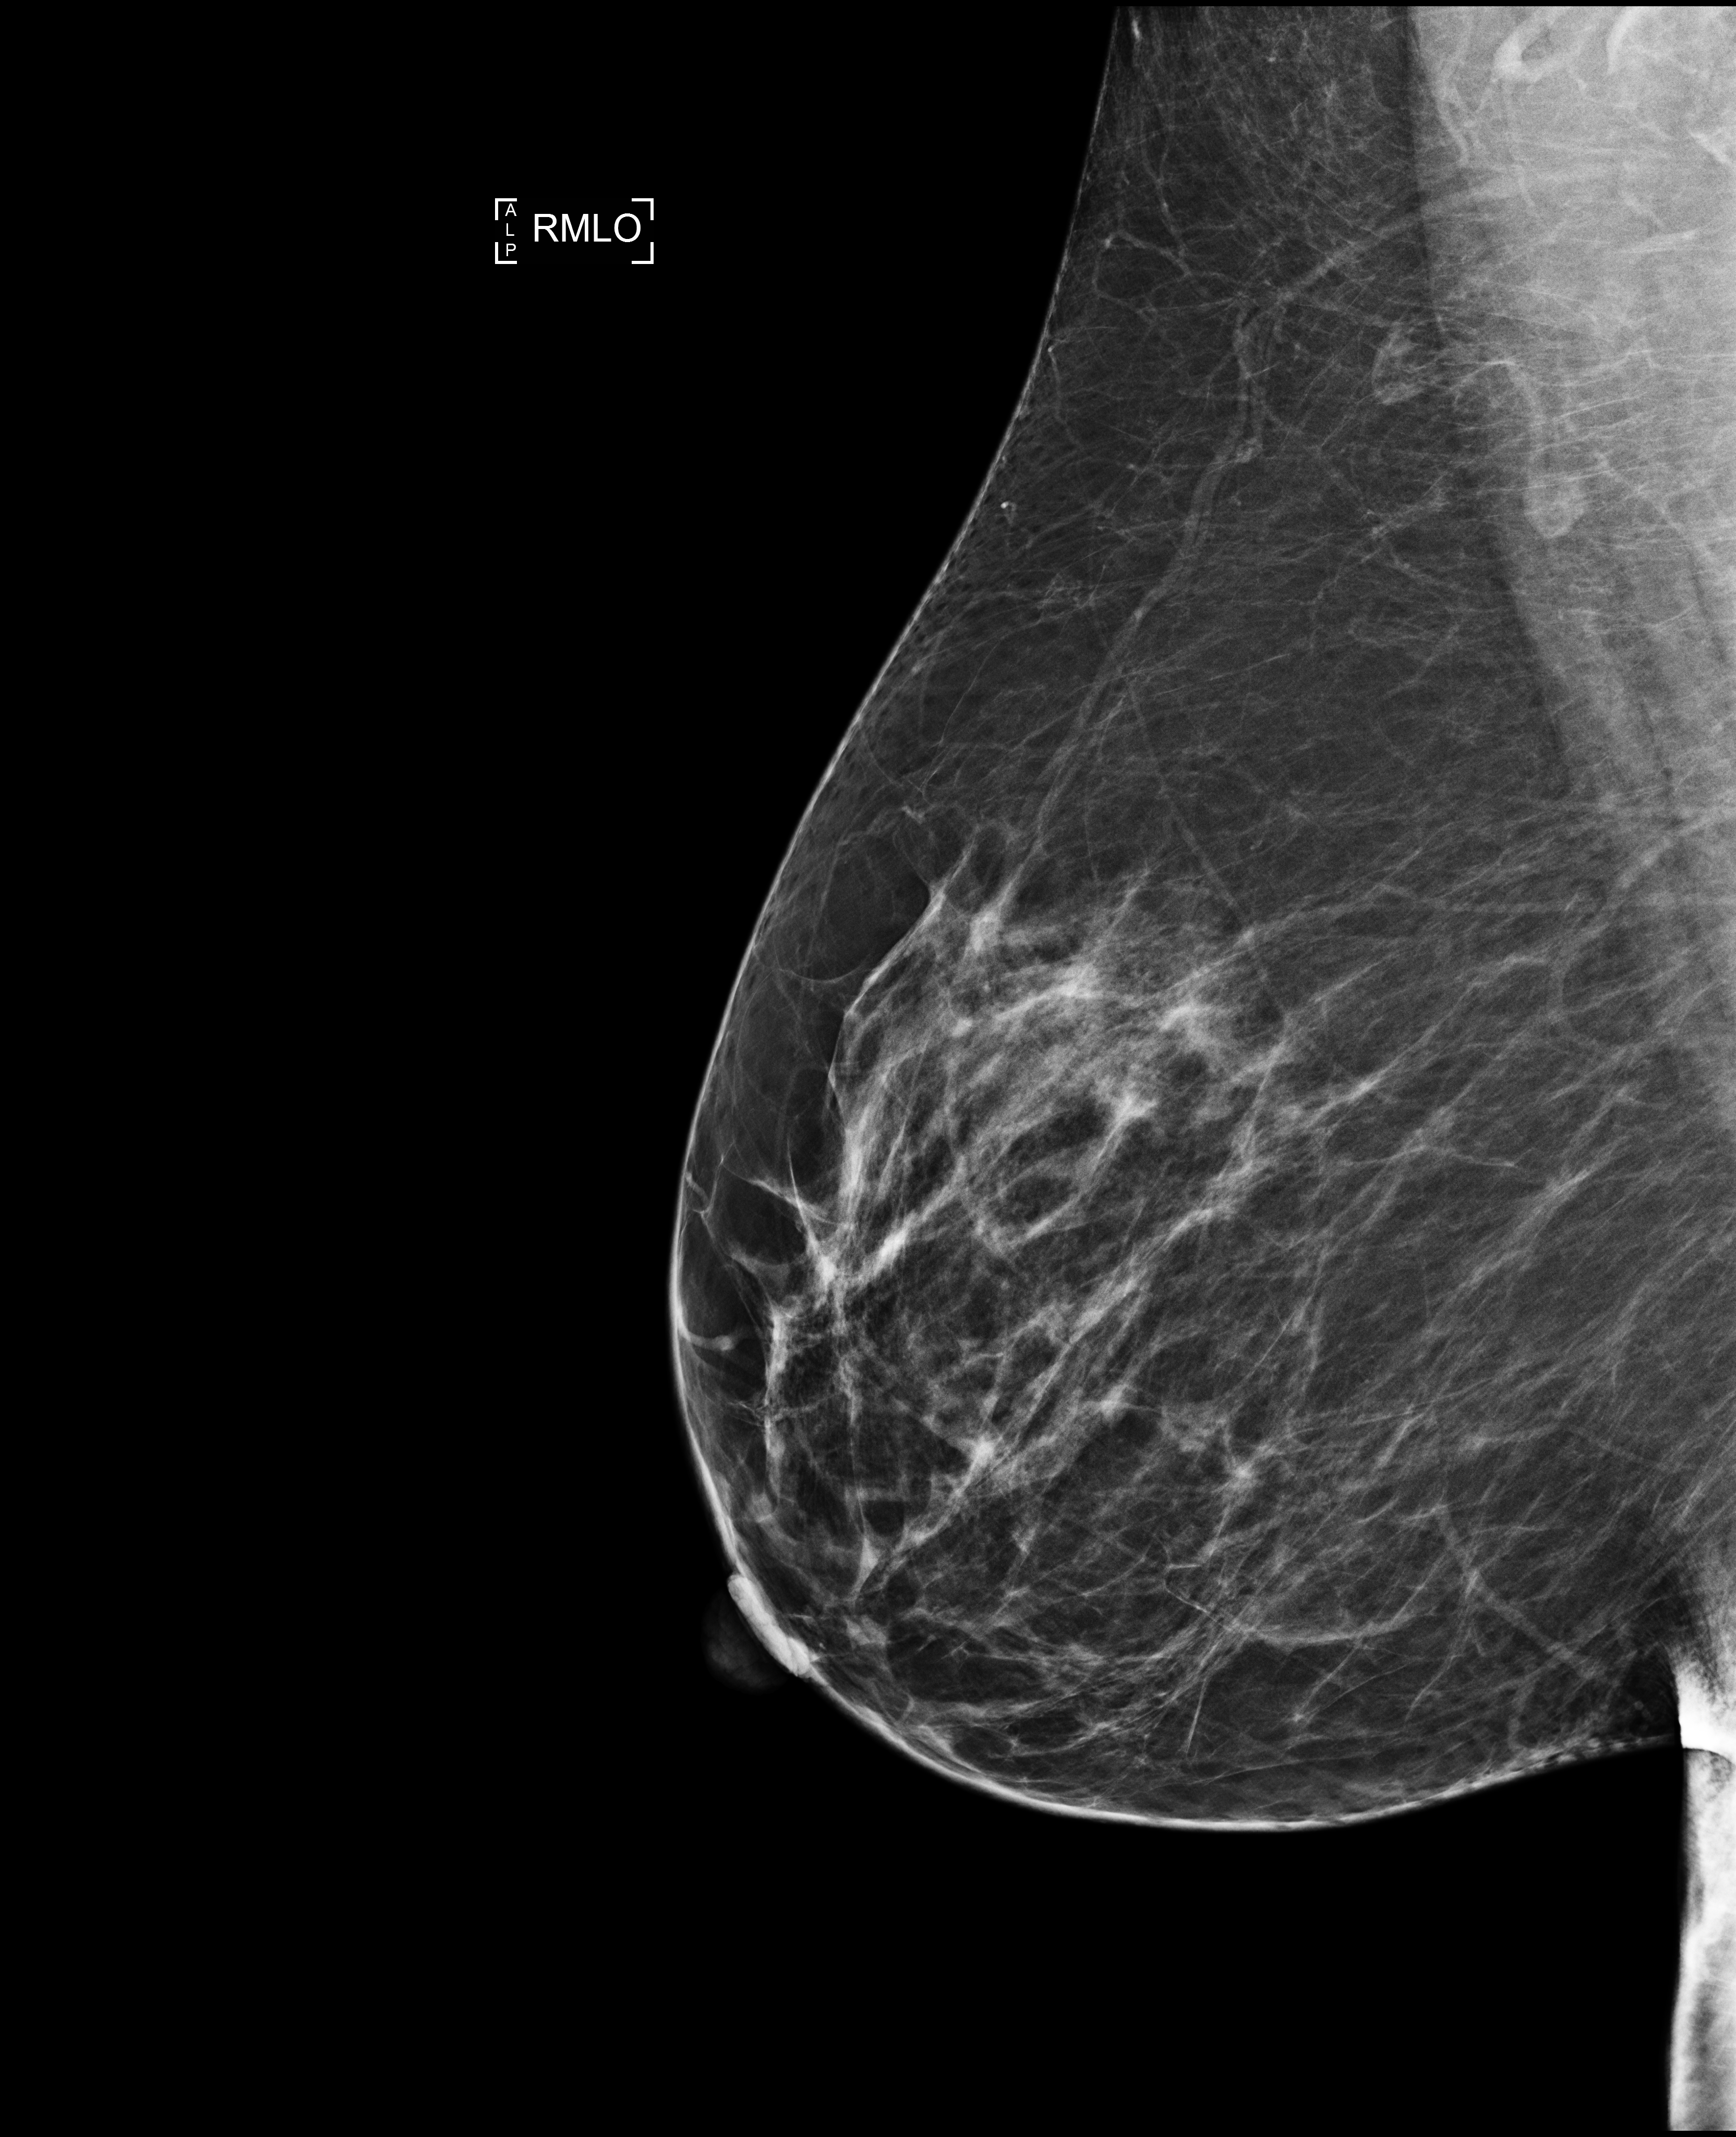
Digital mammogram (FFDM); right breast; MLO view; screening examination; compressed breast thickness 81 mm; system: Selenia Dimensions. Female patient, age 52 years.
- BI-RADS breast density category at the screening exam (both breasts, scale 1–4): 3
- final BI-RADS category for the screening round (tomosynthesis exam, both breasts): category 1
- recall: no recall after this screen